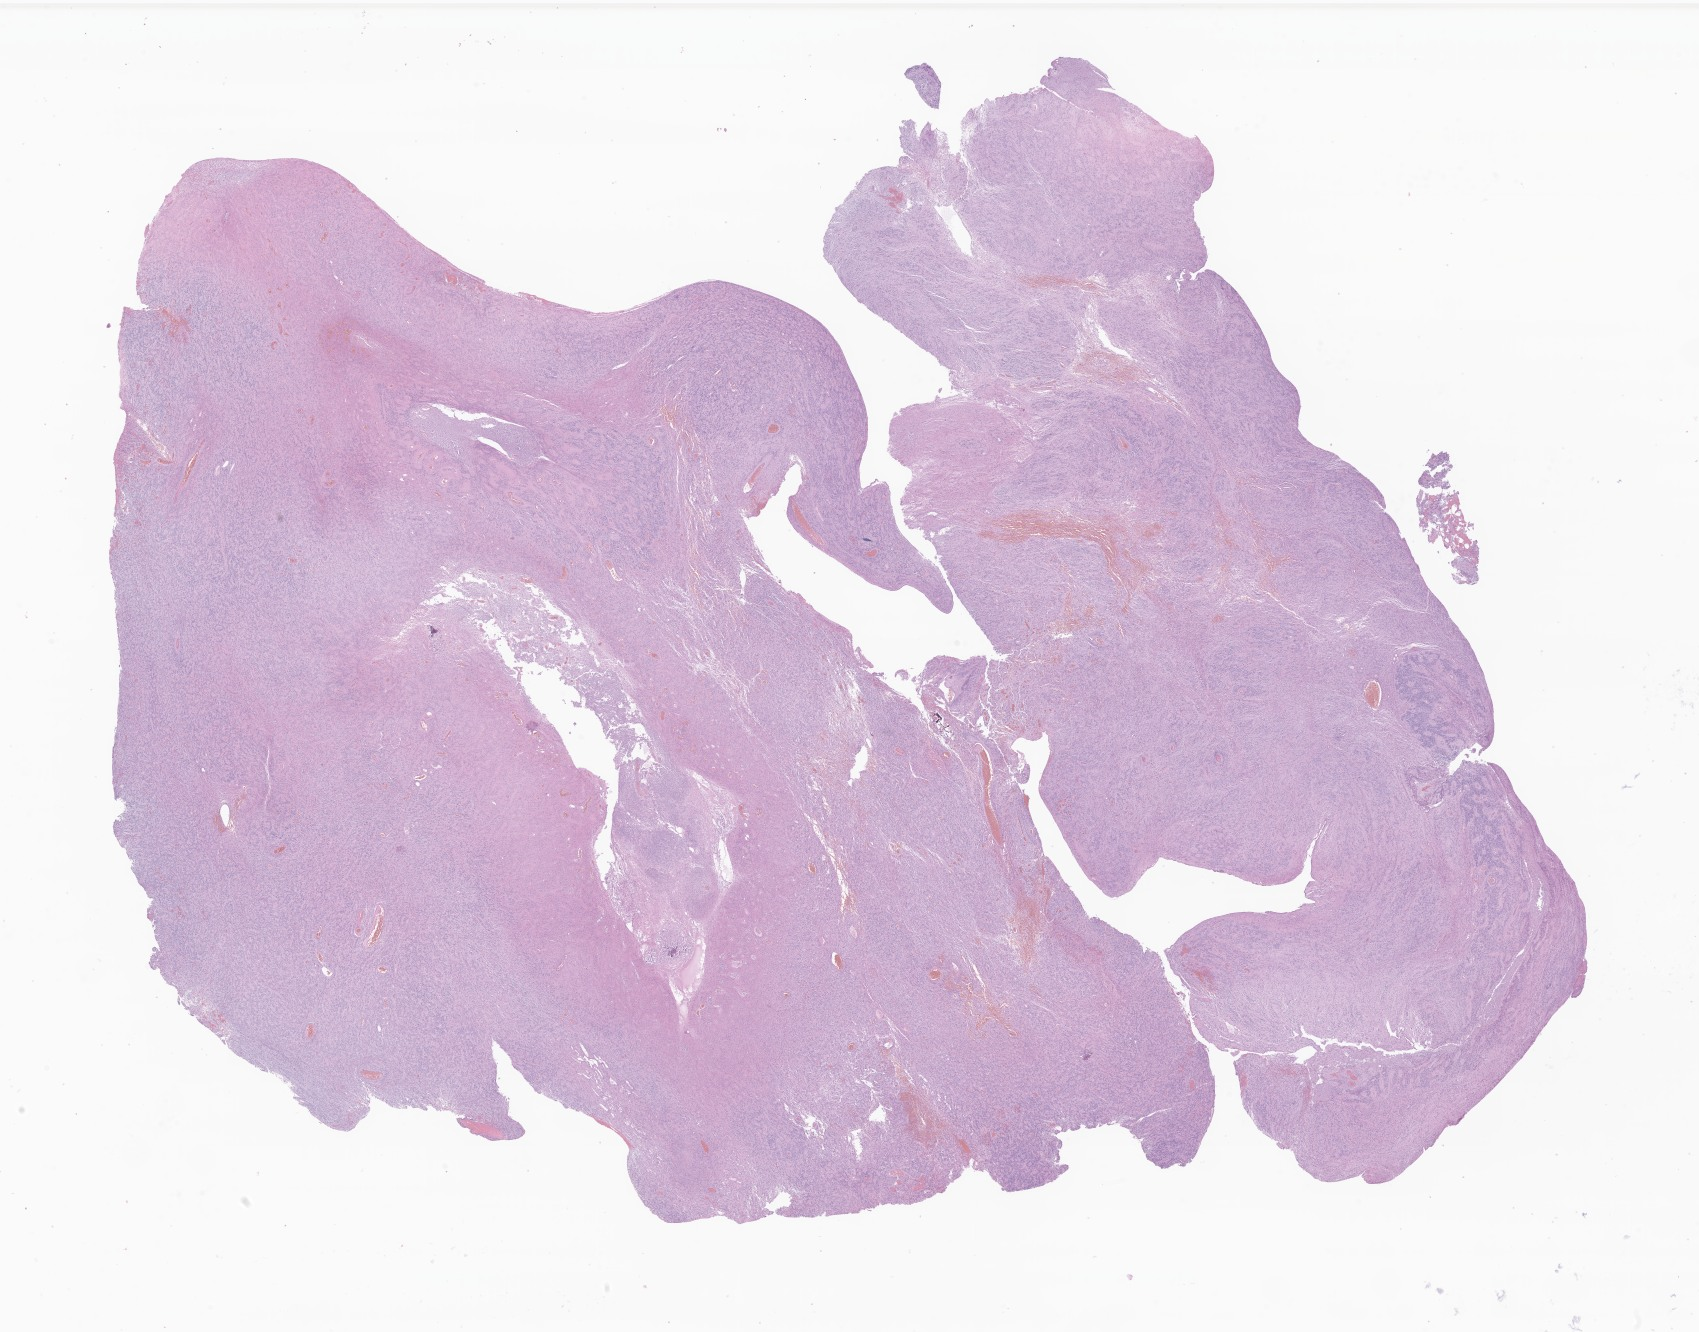
Whole-slide image, H&E stain of tumor tissue from the cerebellum, whole scanned area (about 28.7 x 22.5 mm) shown as a low-resolution overview, formalin-fixed paraffin-embedded section. Male patient, age 79 months.
- diagnosis: Ependymoma, NOS